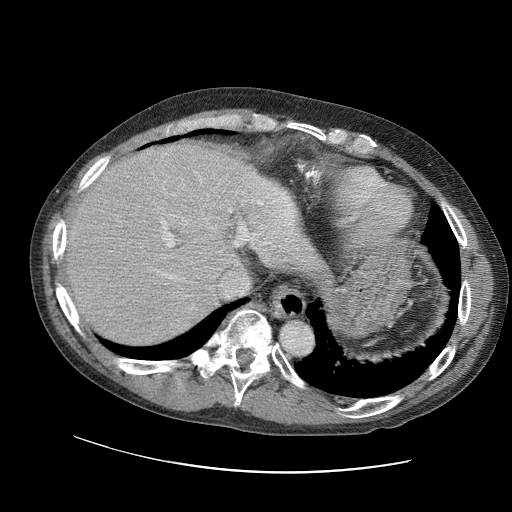
Contrast-enhanced abdominal CT (liver protocol), one axial slice. Slice 80 of 109 in the series (ordered by position). Soft-tissue window (W 400 / L 40 HU). 2.5 mm slice thickness. 512 × 512 image matrix, field of view 400 × 400 mm. From the clinical record (not read from this slice): diagnosis: hepatocellular carcinoma (patient treated with transarterial chemoembolisation; whether this scan precedes or follows treatment is not stated here); TNM stage (as recorded): Stage-IIIC; Child-Pugh class: B; tumour differentiation: well differentiated; tumour nodularity: uninodular.
Structures marked on this image (semi-automatically segmented with operator editing):
- abdominal aorta: bounding box (x1, y1, x2, y2) in pixels: (281, 320, 312, 353)
- liver parenchyma outside the tumour (the mass and vessels are separate outlines, so this box may not span the whole liver): (60, 138, 313, 346)
- liver vessels: (60, 166, 307, 326)